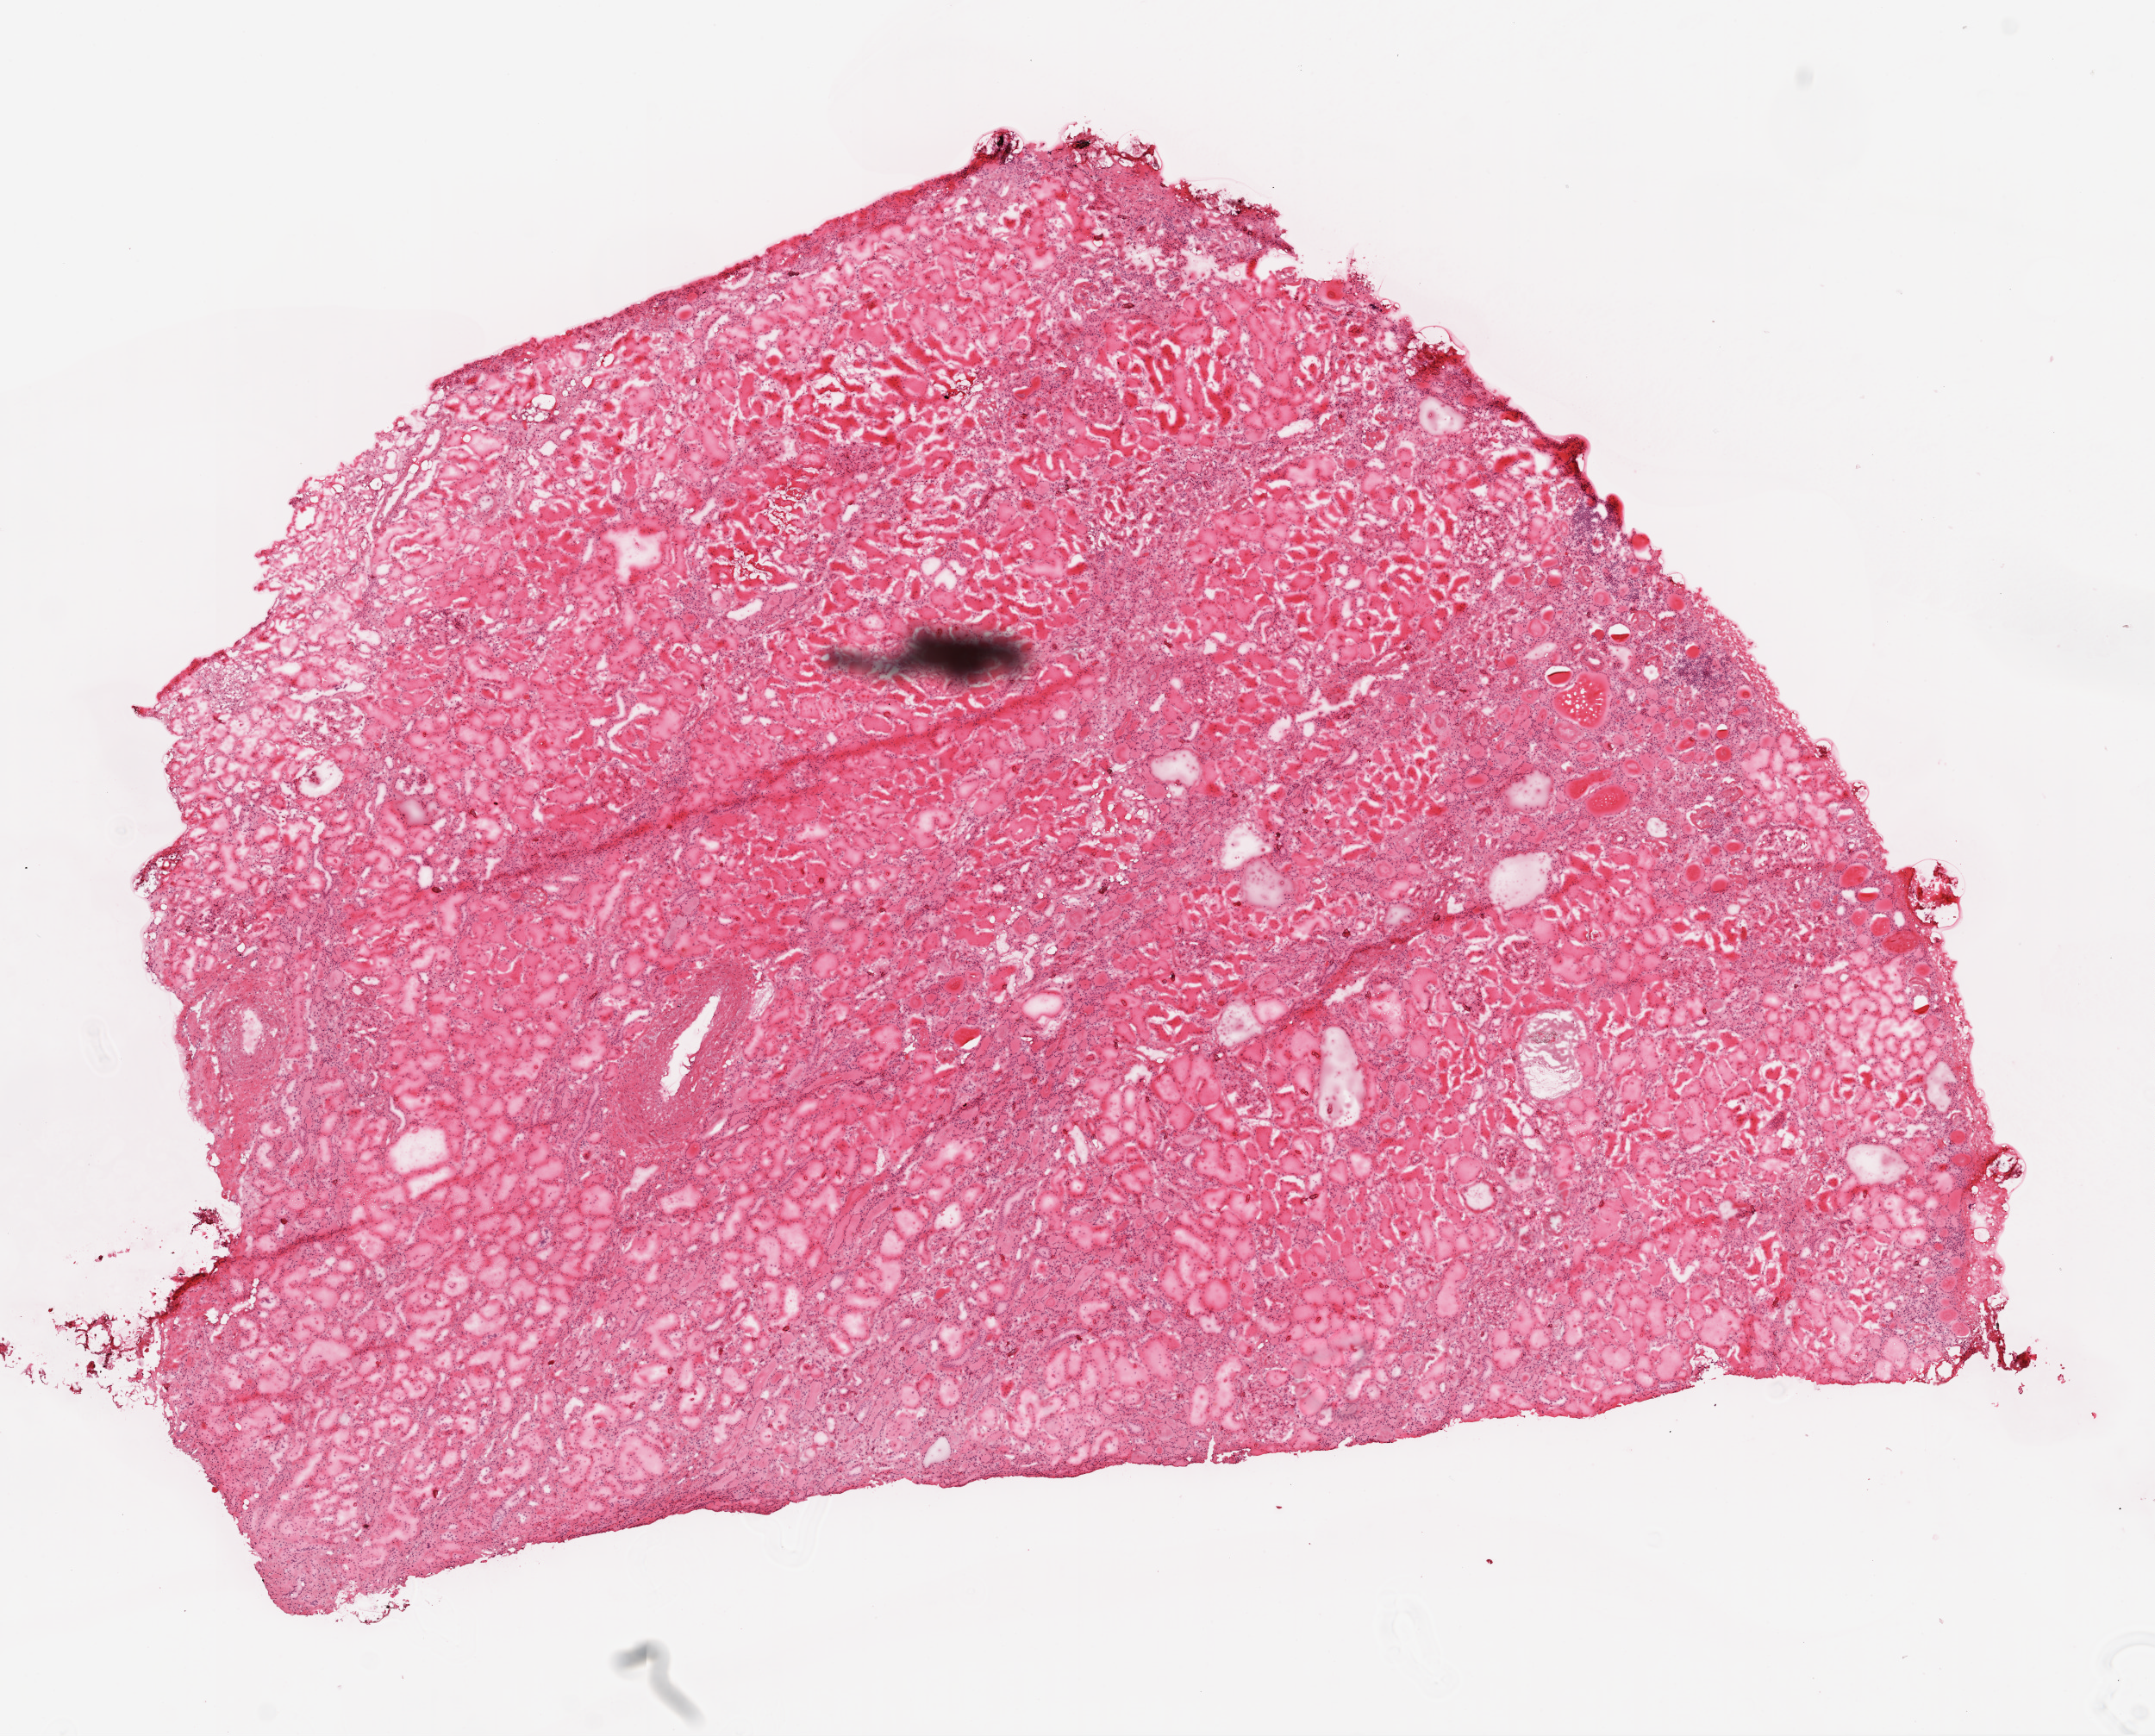
Whole-slide histology image, H&E-stained, low-resolution overview of the scanned area, about 10.0 x 8.1 mm; frozen section from the top of the tissue portion; solid tissue normal (non-tumour tissue) sample from the kidney. Patient: male, age at initial diagnosis 52 years.
- this section: solid tissue normal sample (biorepository sample class)
- patient diagnosis: Clear cell adenocarcinoma, NOS